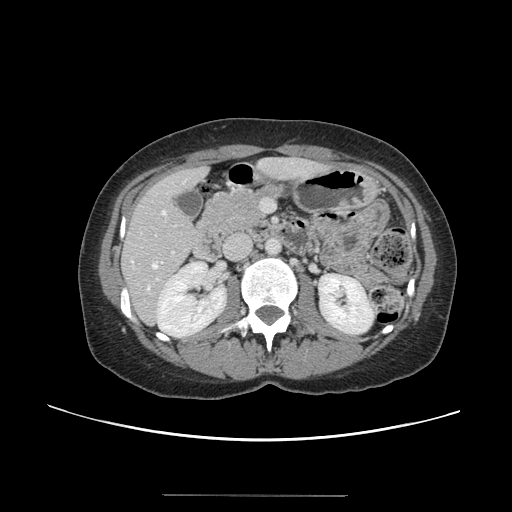
Contrast-enhanced abdominal CT, one axial slice; position 59 of 144 along the scan axis; intravenous contrast given; soft-tissue window (W 400 / L 40 HU); 2.5 mm slice thickness; 512 × 512 image matrix, field of view 380 × 380 mm. Female patient, age 53 years. From the clinical record (not read from this slice): diagnosis: colorectal cancer liver metastases, imaged before liver resection; multiple liver metastases: yes; largest metastasis: 1.1 cm.
Outlined on this slice (expert manual segmentation):
- hepatic veins: box from (x=148, y=211) to (x=166, y=289) px
- liver: (x=124, y=159)–(x=324, y=323)
- planned liver remnant (the part of the liver to remain after resection): (x=124, y=159)–(x=324, y=310)
- portal vein (with intrahepatic branches): (x=156, y=251)–(x=175, y=281)